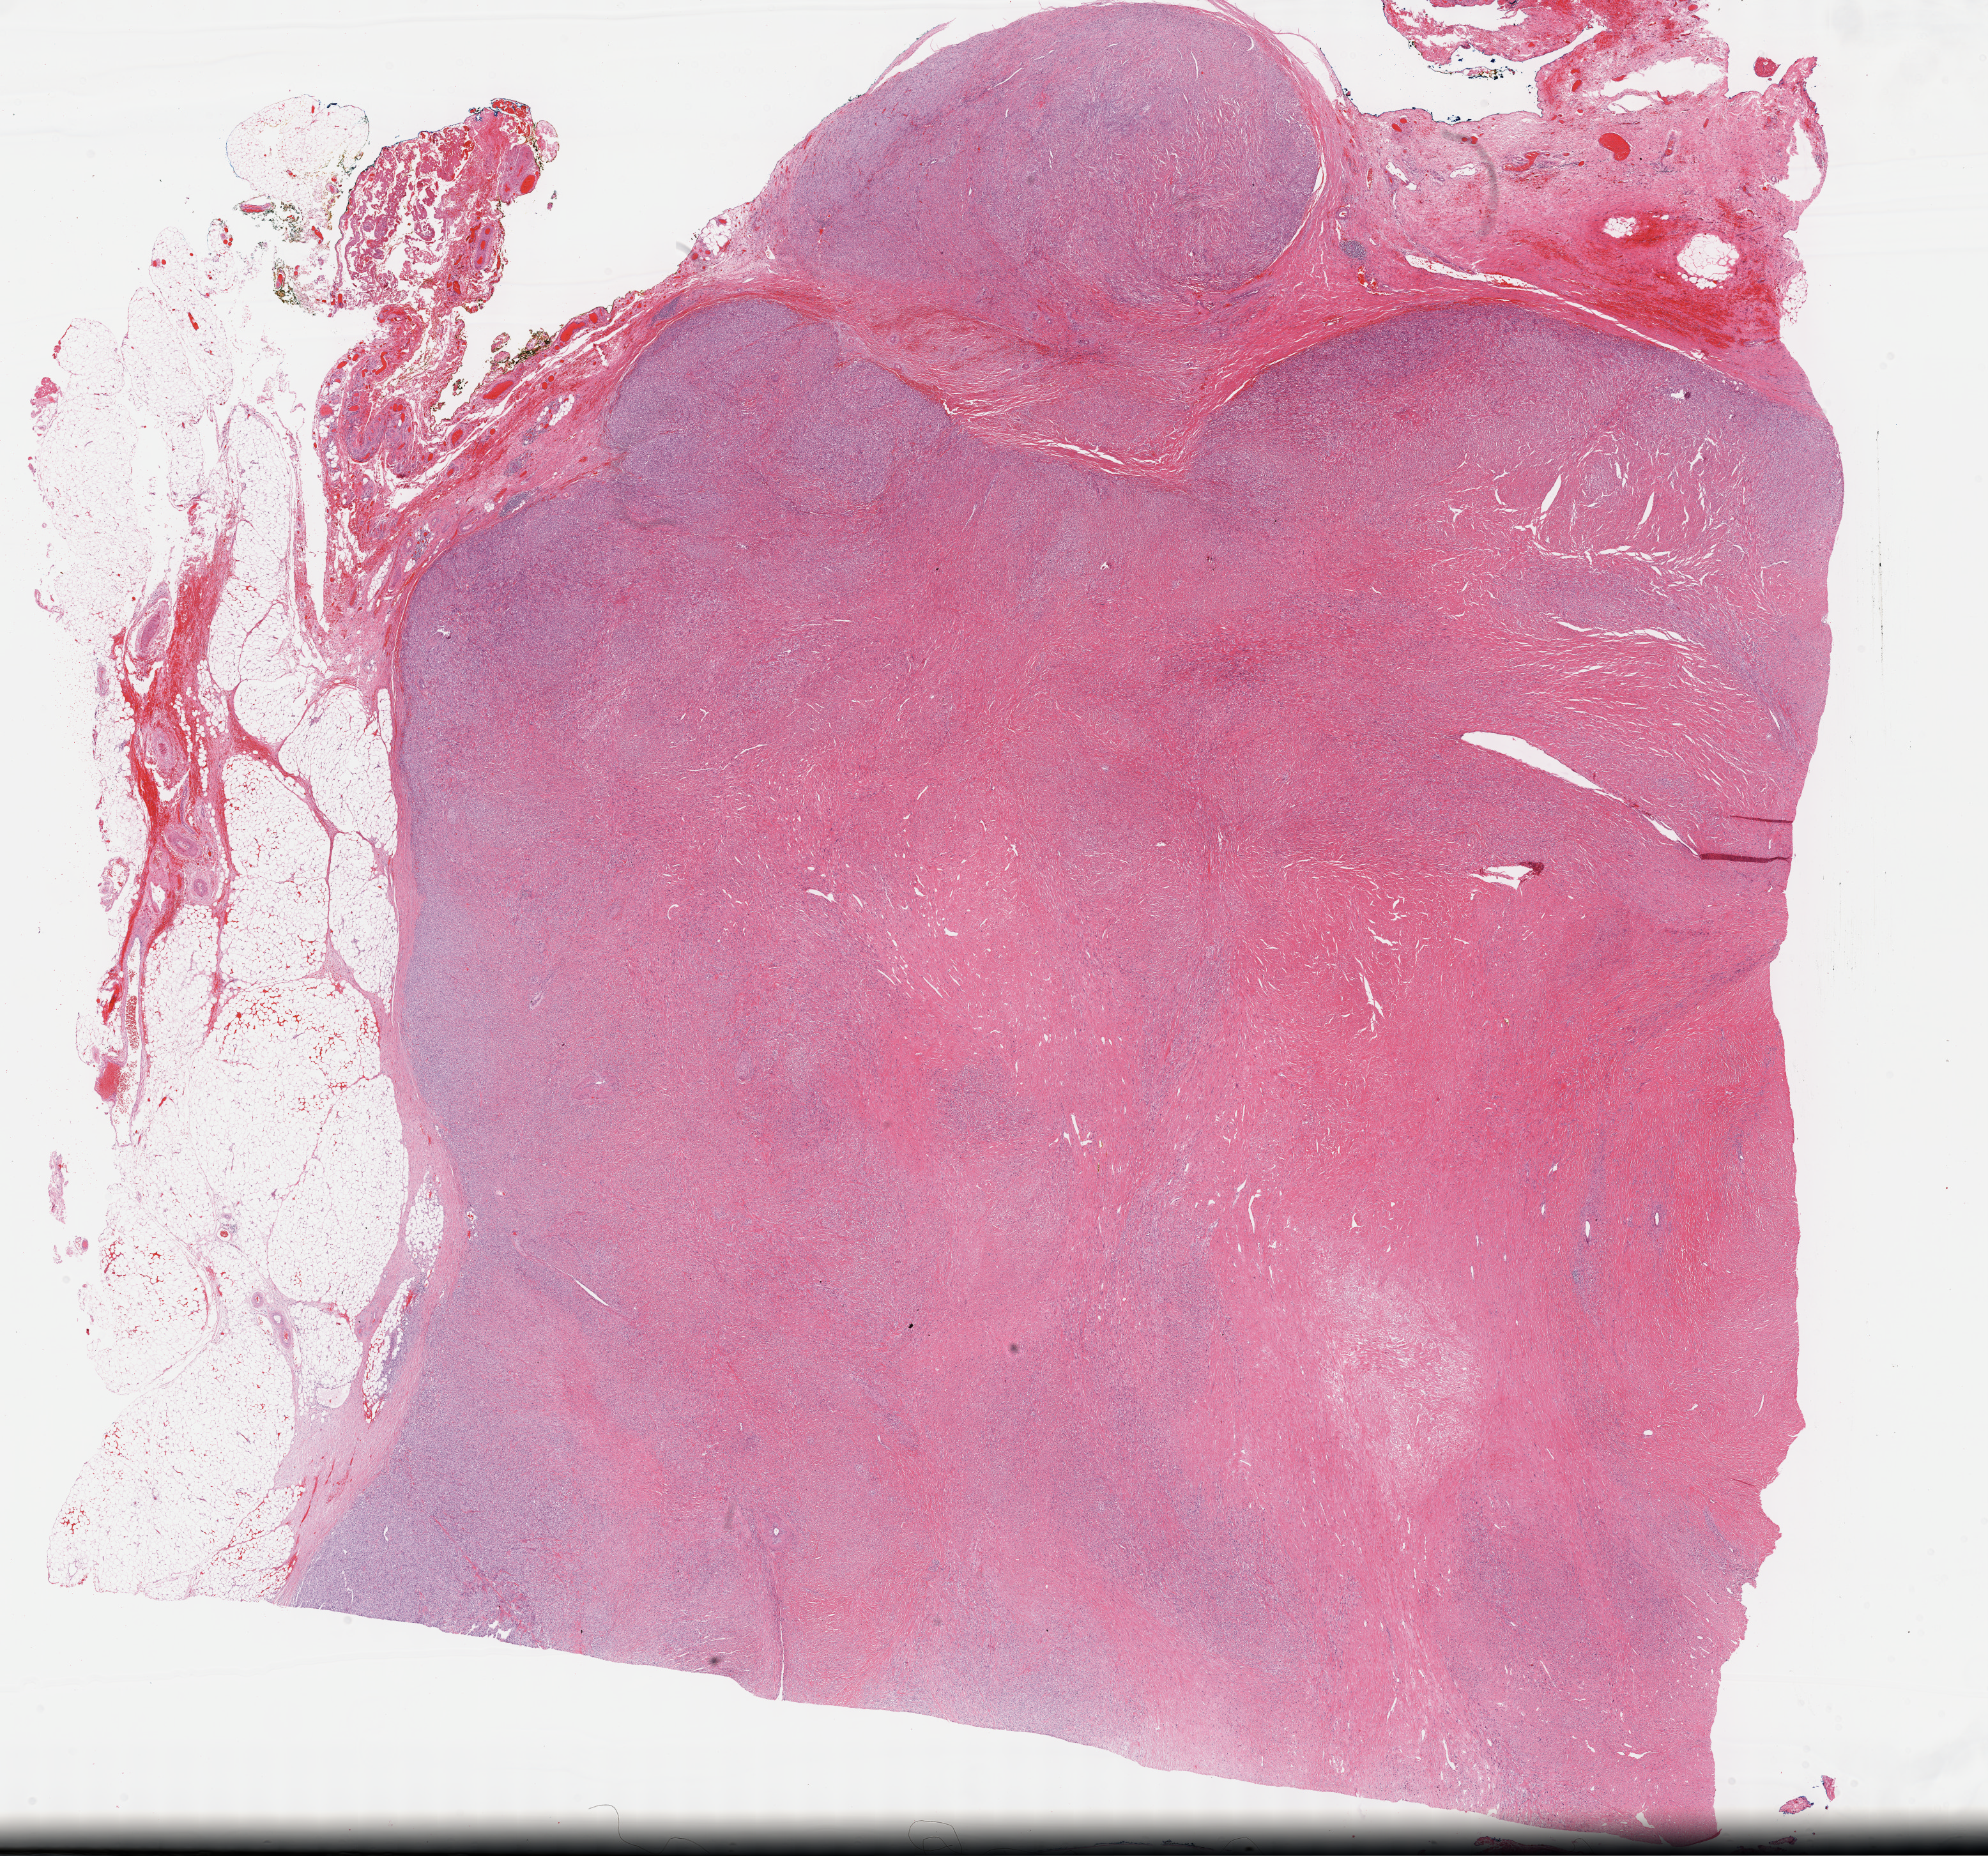
Whole-slide histology image, Hematoxylin and eosin (H&E) stained, low-resolution overview of the scanned area, about 25.2 x 23.5 mm (slide scanned at 40x). Formalin-fixed paraffin-embedded (FFPE) diagnostic section. Sample: primary tumour, retroperitoneum and peritoneum. Patient: female, age at initial diagnosis 66 years.
Histologic diagnosis: Dedifferentiated liposarcoma (retroperitoneum).